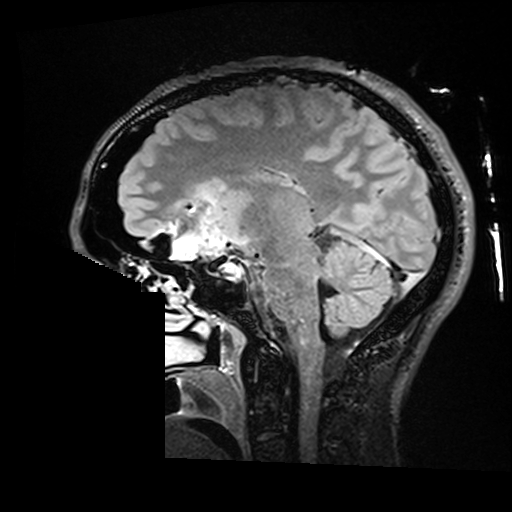
Brain MRI from a brain-tumour surgery series, one sagittal slice. Position 94 of 176 along the scan axis. T2 FLAIR. 512 × 512 image matrix, field of view 250 × 250 mm. Case-level facts recorded for this patient, not image findings: histopathology: Astrocytoma; WHO grade: 2; IDH mutation: yes; tumour location: Right Insular.
Outlined on this slice (manually delineated by an expert):
- residual tumour: box from (x=200, y=180) to (x=226, y=204) px